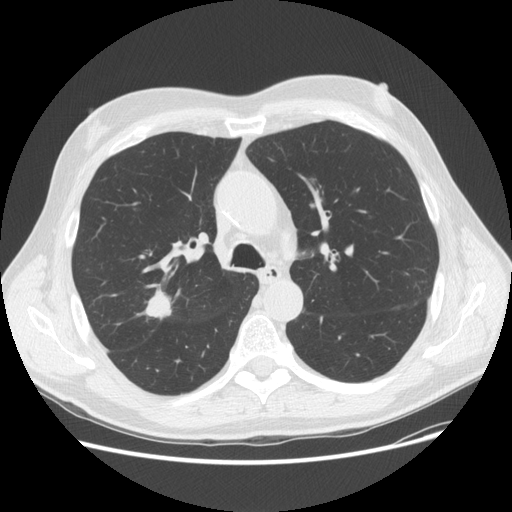
Low-dose screening chest CT, one axial slice; 120 kVp; lung window (W 1500 / L -600 HU); 512 × 512 image matrix, field of view 380 × 380 mm.
Structures marked on this image (expert manual segmentation):
- lesion 1 (tumor, upper lobe of right lung): bounding box (x1, y1, x2, y2) in pixels: (144, 288, 177, 320)